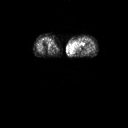
FDG PET of an extremity soft-tissue mass (from a PET/CT study), one axial slice. Position 13 of 91 along the scan axis. 3.27 mm slice thickness. 128 × 128 image matrix, field of view 700 × 700 mm. Female patient, age 74 years. From the clinical record (not read from this slice): histological type: pleomorphic leiomyosarcoma; grade: high; site of the primary tumour: left thigh.
Annotated regions visible in this slice (expert contour drawn on MRI and transferred to this co-registered scan by the dataset authors):
- gross tumour volume including surrounding oedema: bounding box [x1, y1, x2, y2] px = [70, 40, 86, 53]
- gross tumour volume (mass): [70, 49, 75, 53]